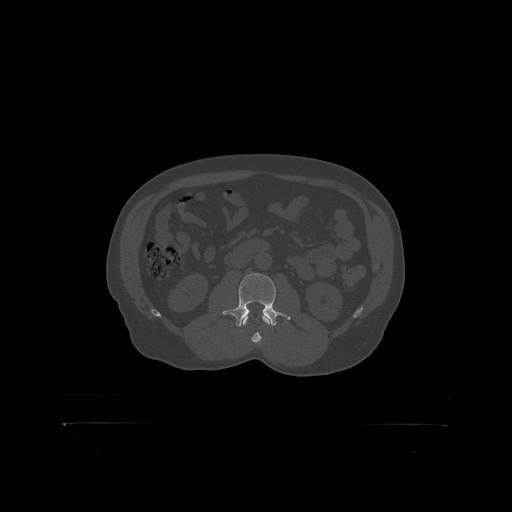
CT including the spine, one axial slice; slice 275 of 399 in the series (ordered by position); reconstruction kernel STANDARD; 120 kVp; bone window (W 1800 / L 400 HU); 512 × 512 image matrix, field of view 650 × 650 mm. Patient: male, 46 years. From the clinical record (not read from this slice): primary cancer: skin.
Outlined on this slice (semi-automatically segmented with operator editing):
- L2 vertebra: box from (x=244, y=315) to (x=249, y=319) px
- L3 vertebra: (x=227, y=273)–(x=281, y=319)